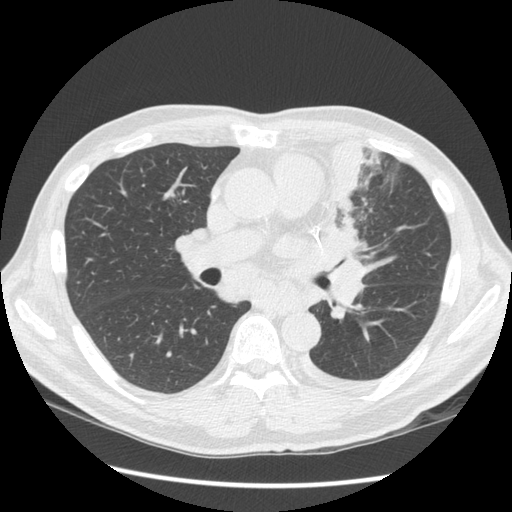
Low-dose screening chest CT, one axial slice. Position 80 of 136 along the scan axis. Lung window (W 1500 / L -600 HU). 2.5 mm slice thickness. 512 × 512 image matrix.
Outlined on this slice (outlined manually by an expert reader):
- lesion 1 (tumor, upper lobe of left lung): box from (x=323, y=141) to (x=367, y=261) px